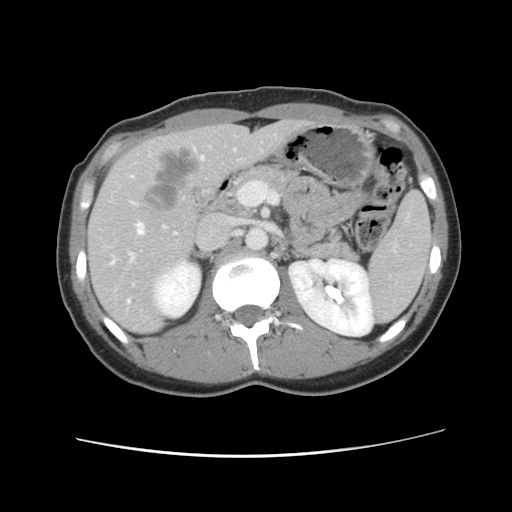
Contrast-enhanced abdominal CT, one axial slice; slice 55 of 134 in the series (ordered by position); 120 kVp; intravenous contrast given; soft-tissue window (W 400 / L 40 HU); 2.5 mm slice thickness; 512 × 512 image matrix, field of view 339 × 339 mm. Female patient, age 33 years. Case-level facts recorded for this patient, not image findings: diagnosis: colorectal cancer liver metastases, imaged before liver resection; multiple liver metastases: yes; largest metastasis: 4.5 cm; disease in both lobes: yes.
Outlined on this slice (expert manual segmentation):
- hepatic veins: bounding box (x1, y1, x2, y2) in pixels: (112, 156, 205, 303)
- liver: (89, 121, 309, 333)
- planned liver remnant (the part of the liver to remain after resection): (90, 120, 308, 333)
- portal vein (with intrahepatic branches): (113, 225, 179, 291)
- liver metastasis: (142, 147, 200, 211)